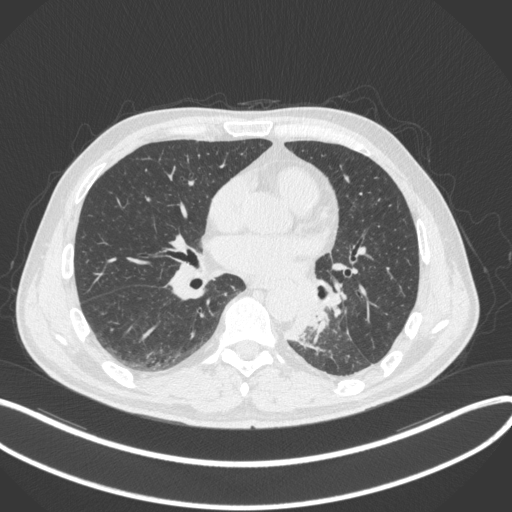
Chest CT, one axial slice; slice 154 of 328 in the series (ordered by position); 120 kVp; lung window (W 1500 / L -600 HU); 1 mm slice thickness; 512 × 512 image matrix, field of view 400 × 400 mm. Patient: male, 59 years. From the clinical record (not read from this slice): clinical TNM (as recorded): T2a N2 M0.
Structures marked on this image (bounding box drawn by a radiologist):
- lung tumour (recorded histology: squamous cell carcinoma): box from (x=288, y=300) to (x=334, y=348) px